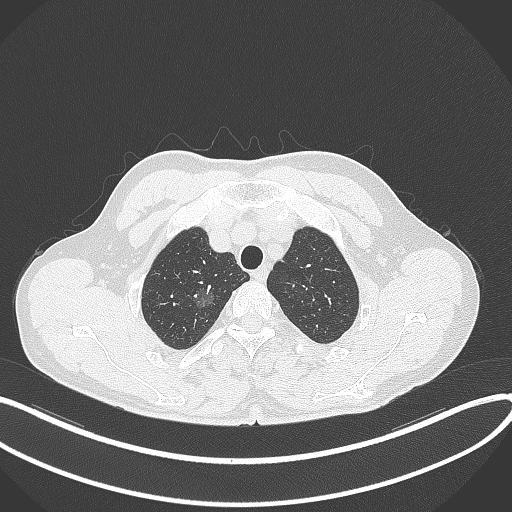
Chest CT, one axial slice. Slice 324 of 407 in the series (ordered by position). Reconstruction kernel B70f. Lung window (W 1500 / L -600 HU). 1 mm slice thickness. 512 × 512 image matrix. Patient: male, 58 years. From the clinical record (not read from this slice): clinical TNM (as recorded): T1c N0 M0; histopathological grade: G1-2.
Outlined on this slice (bounding box drawn by a radiologist):
- lung tumour (recorded histology: adenocarcinoma): bounding box [x1, y1, x2, y2] px = [188, 281, 215, 313]